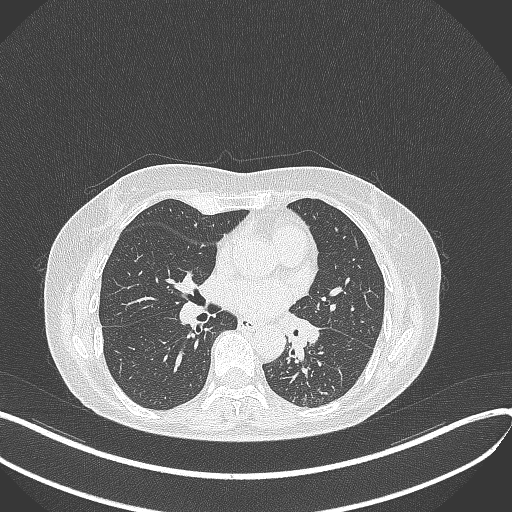
Chest CT, one axial slice. Position 208 of 429 along the scan axis. Reconstruction kernel B70f. 100 kVp. Lung window (W 1500 / L -600 HU). 1 mm slice thickness. 512 × 512 image matrix, field of view 400 × 400 mm. Patient: female, 63 years. From the clinical record (not read from this slice): clinical TNM (as recorded): T1b N0 M0.
Outlined on this slice (rectangle marked by the reading radiologist):
- lung tumour (recorded histology: adenocarcinoma): box from (x=284, y=315) to (x=323, y=359) px